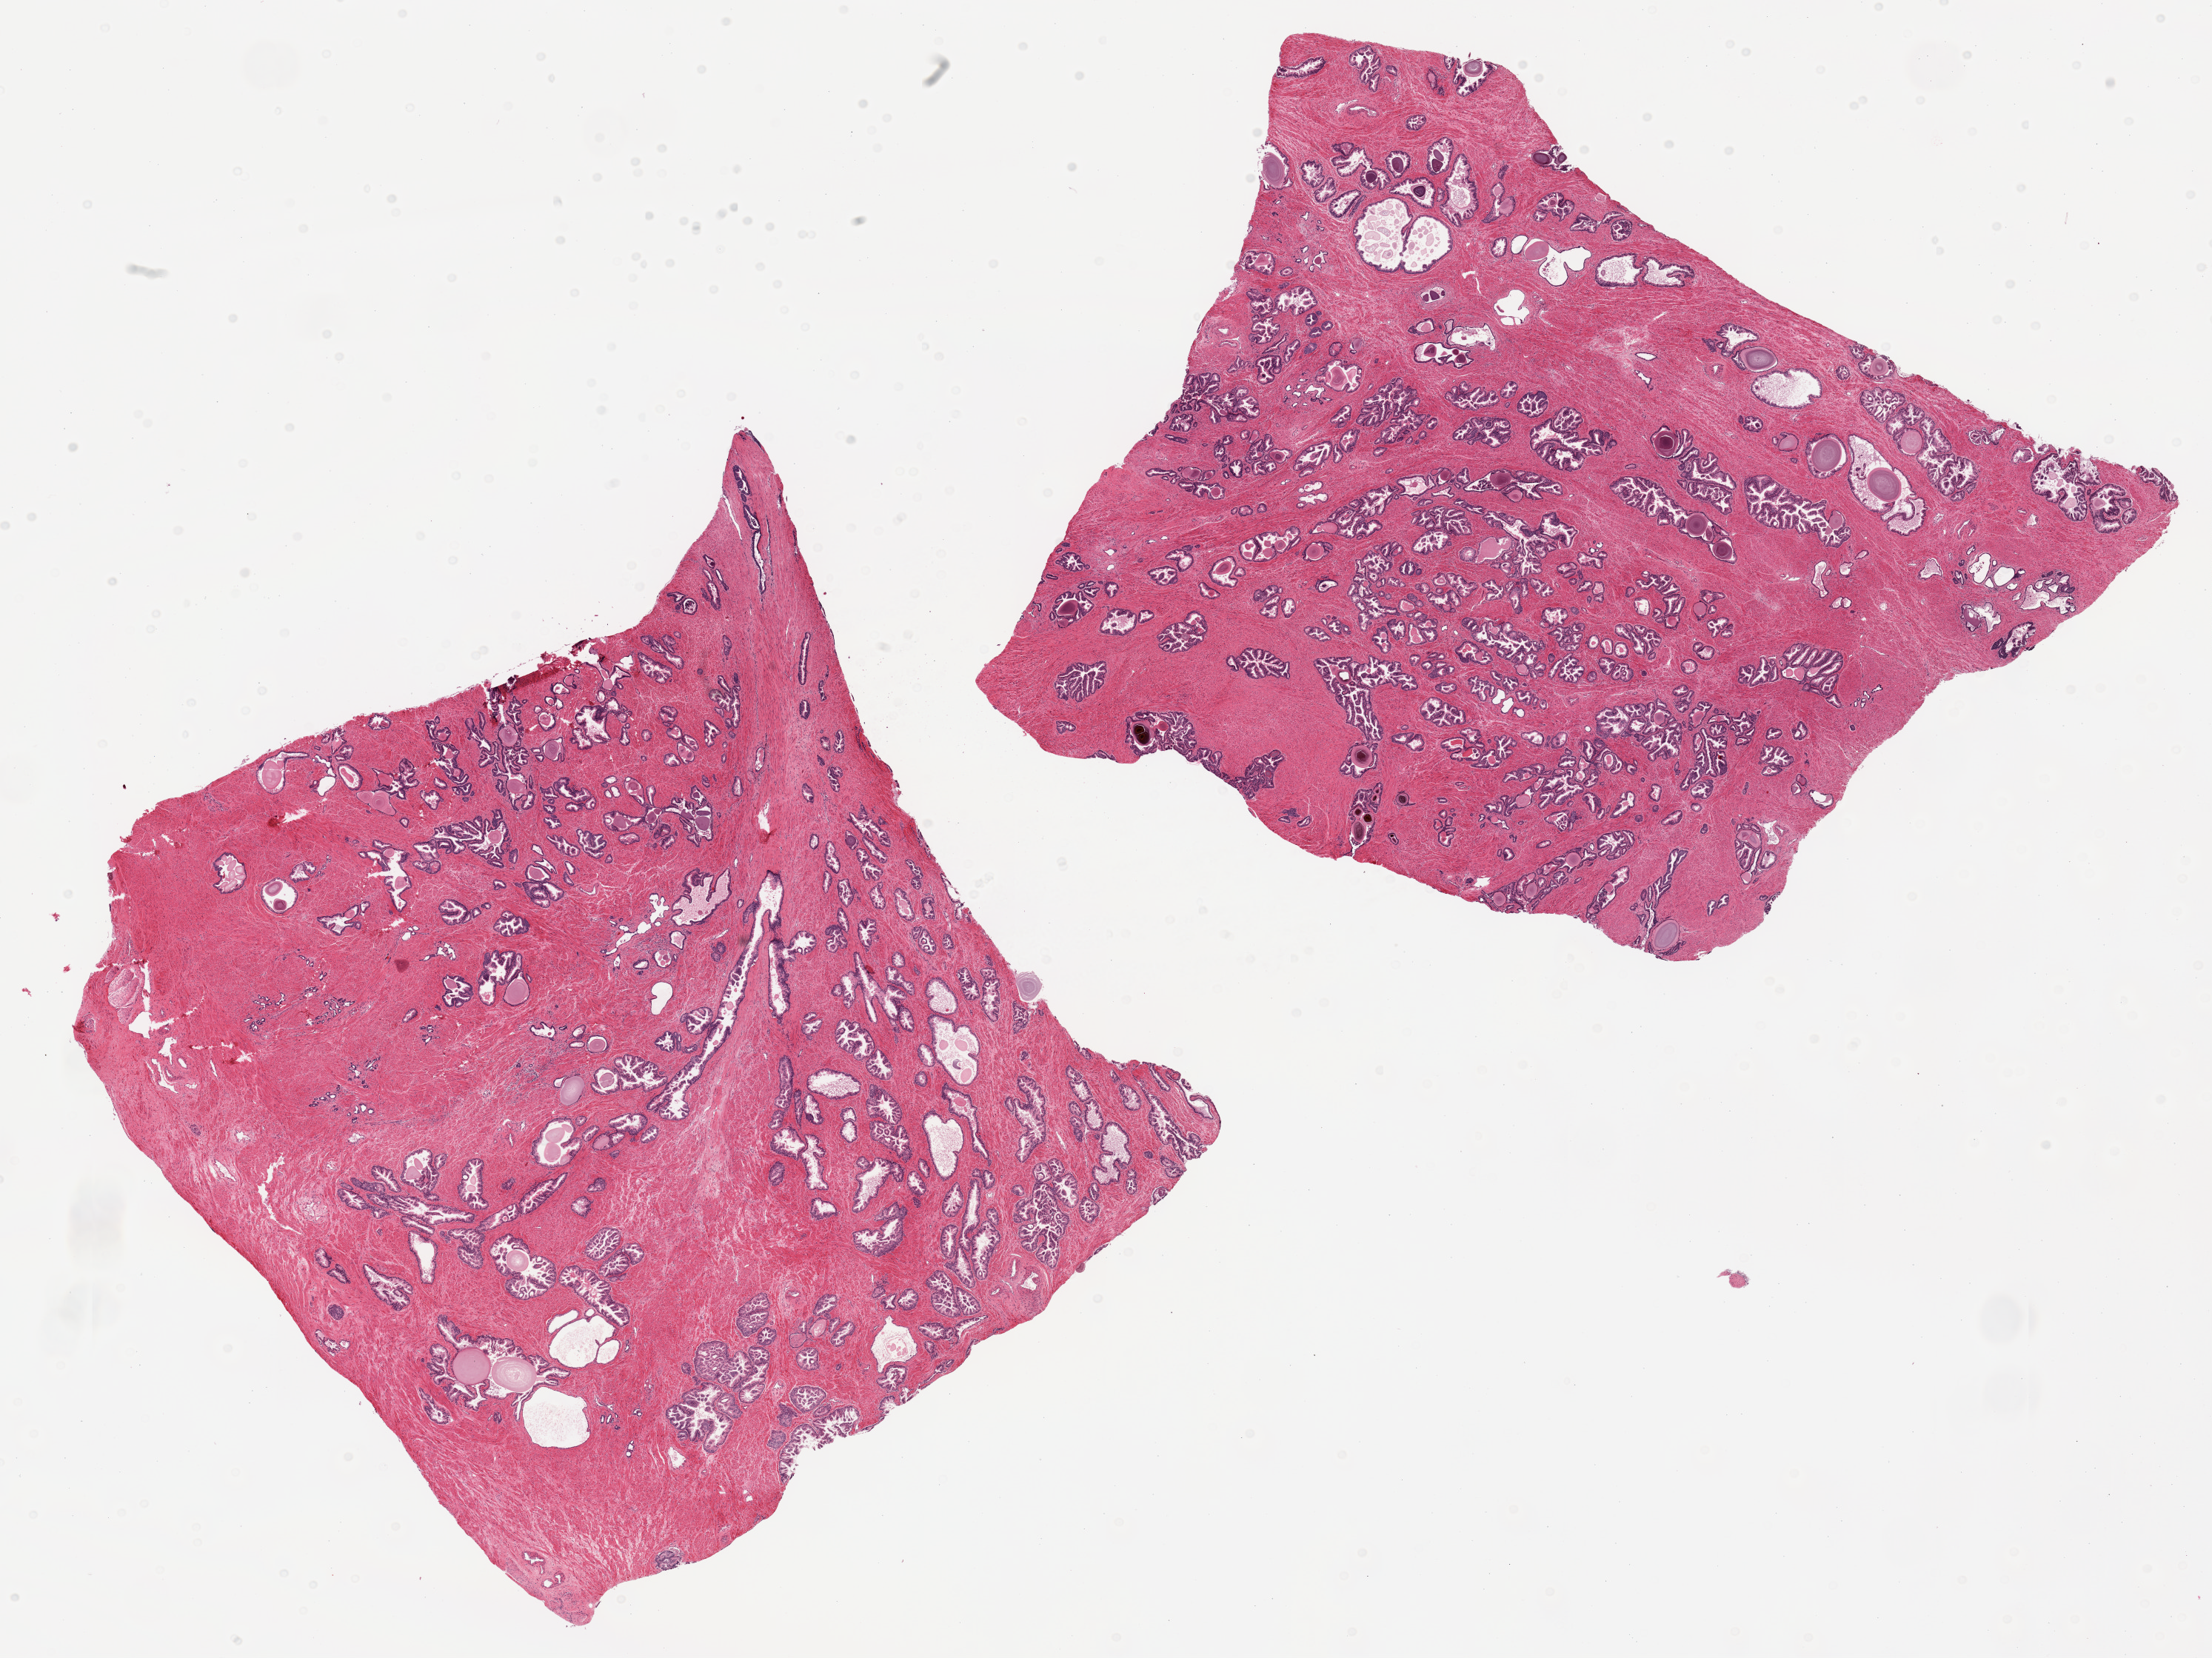
Digitized haematoxylin and eosin-stained section, whole scanned area (about 23.6 x 17.7 mm) shown as a low-resolution overview; PAXgene-fixed, paraffin-embedded tissue; target tissue: prostate; donor tissue sample. Donor: male.
- review note (as recorded): 2 pieces